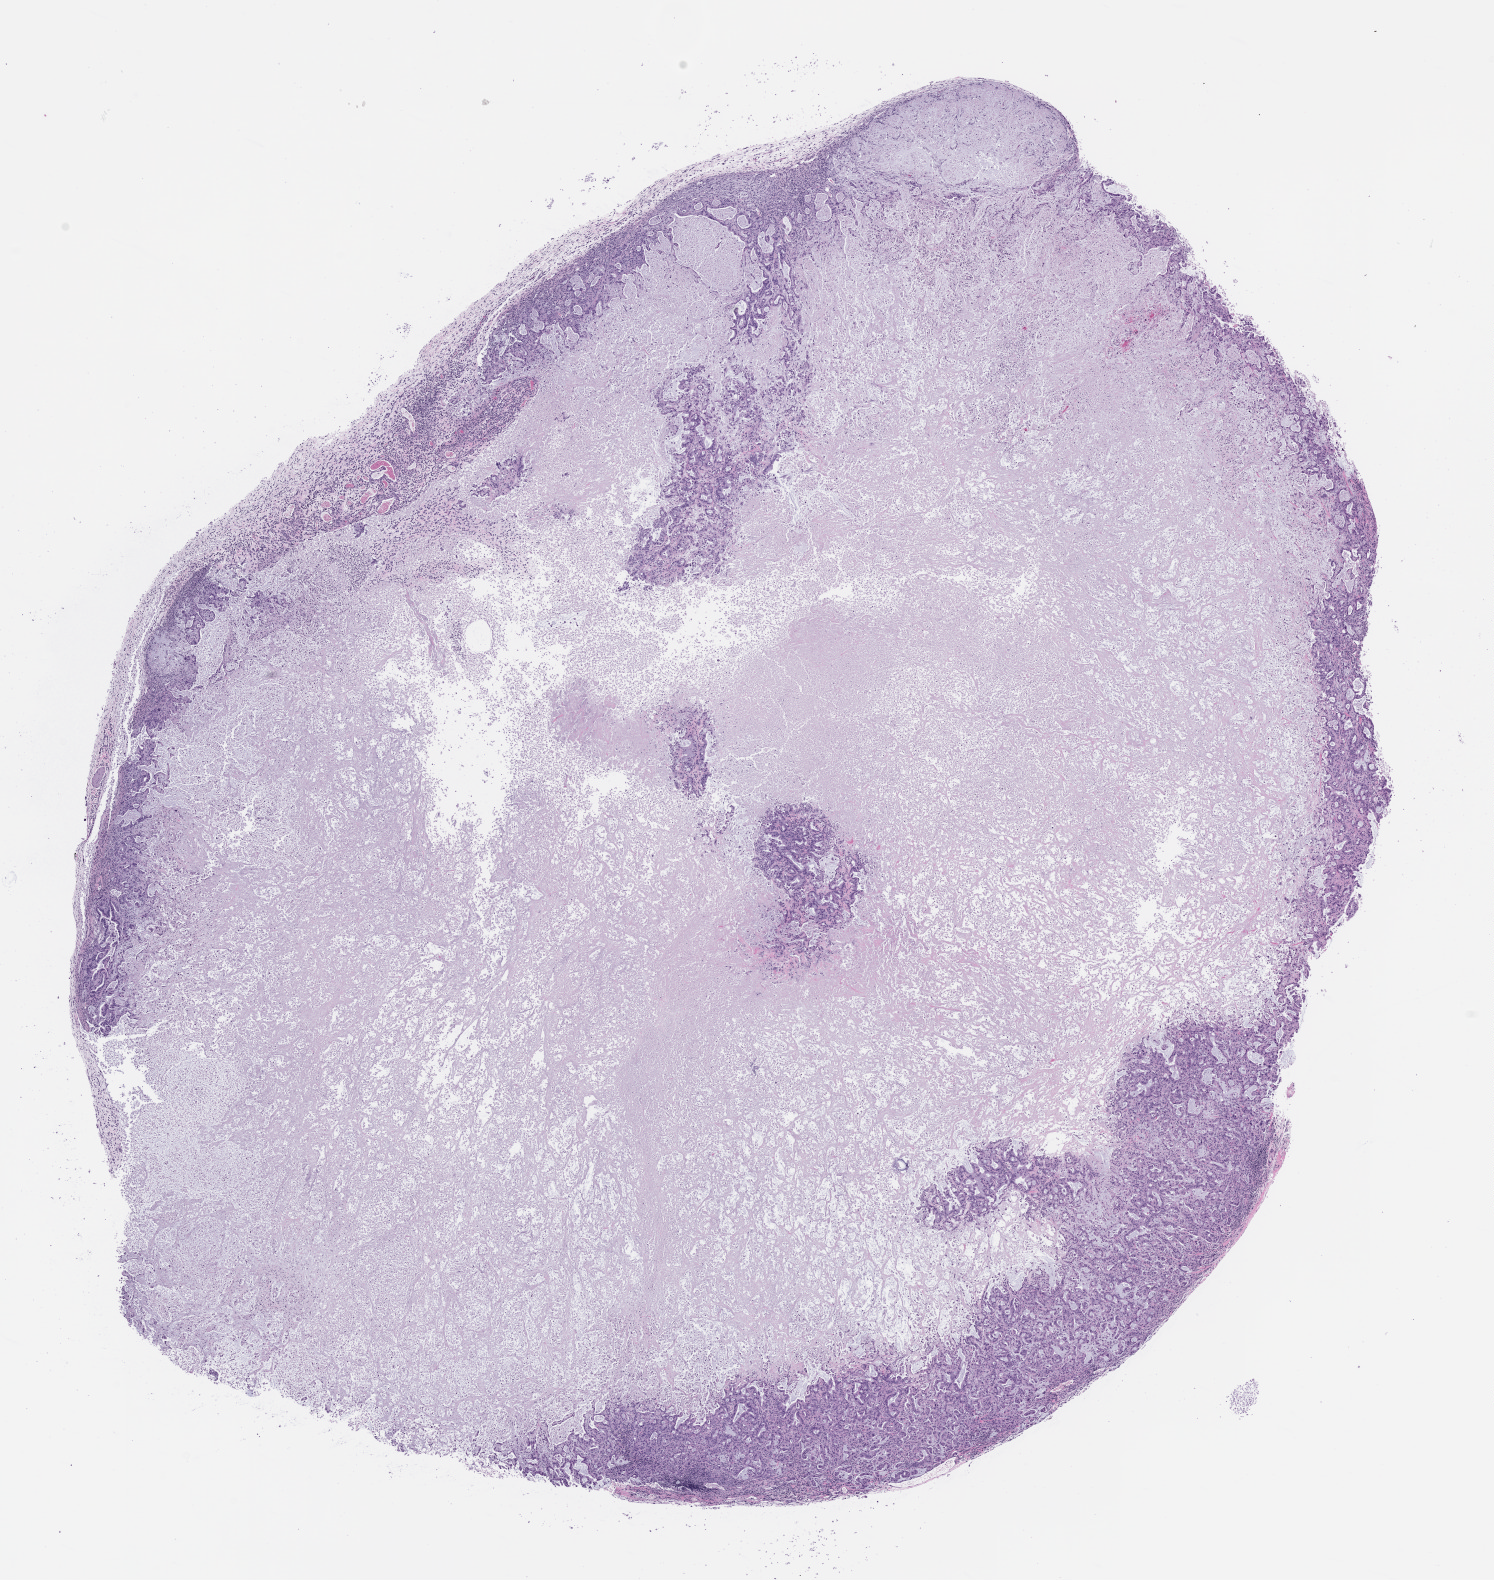
Whole-slide image, H&E: patient-derived xenograft (human tumor grown in a mouse), passage 2 — shown as a low-resolution overview of the whole scanned area (about 12.0 x 12.7 mm). Formalin-fixed, paraffin-embedded (FFPE) tissue. Originating tumor site category: pancreas.
Originating patient diagnosis: Pancreatic Adenocarcinoma.